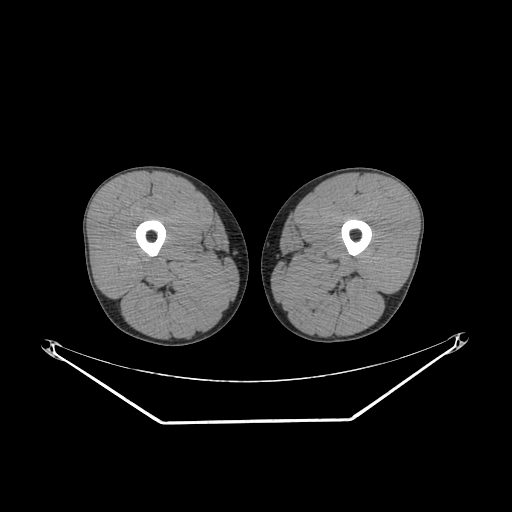
CT of an extremity soft-tissue mass (from a PET/CT study), one axial slice; reconstruction kernel SOFT; soft-tissue window (W 400 / L 40 HU); 3.75 mm slice thickness; 512 × 512 image matrix. Male patient. From the clinical record (not read from this slice): histological type: extraskeletal osteosarcoma; grade: high; site of the primary tumour: left adductur.
Annotated regions visible in this slice (expert contour drawn on MRI and transferred to this co-registered scan by the dataset authors):
- gross tumour volume (mass): bounding box <283,251,360,284> (left, top, right, bottom; pixels)